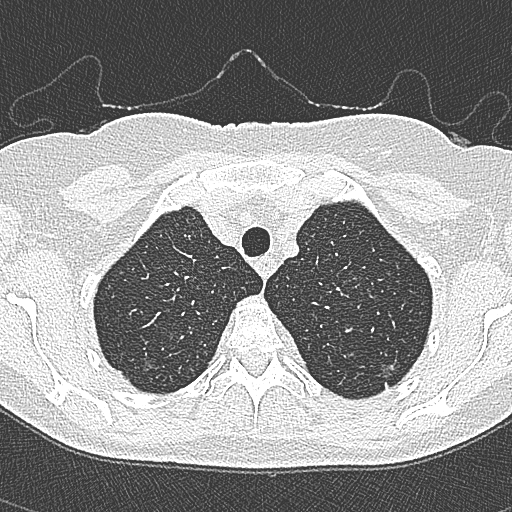
Axial slice from a low-dose chest CT screening exam; second screening round (one year after baseline); lung window (W 1500 / L -600 HU); 1 mm slice thickness. Female, age 65 years at enrolment. Current smoker at enrolment.
• Expert reader's lesion annotation, bounding box [x1, y1, x2, y2] px = [368, 346, 413, 389].
• The screening reader recorded 4 non-calcified nodules or masses ≥4 mm on this exam (left upper lobe, left upper lobe, left upper lobe, right lower lobe); which of them this box marks is not recorded.
• Official screen result: positive, change unspecified: nodule(s) >= 4 mm or enlarging nodule(s), mass(es), or other non-specific abnormalities suspicious for lung cancer.
• Lung cancer was diagnosed 54 days after this screen: bronchiolo-alveolar carcinoma, non-mucinous, left upper lobe, stage IA (AJCC 6th edition), 10 mm at pathology.